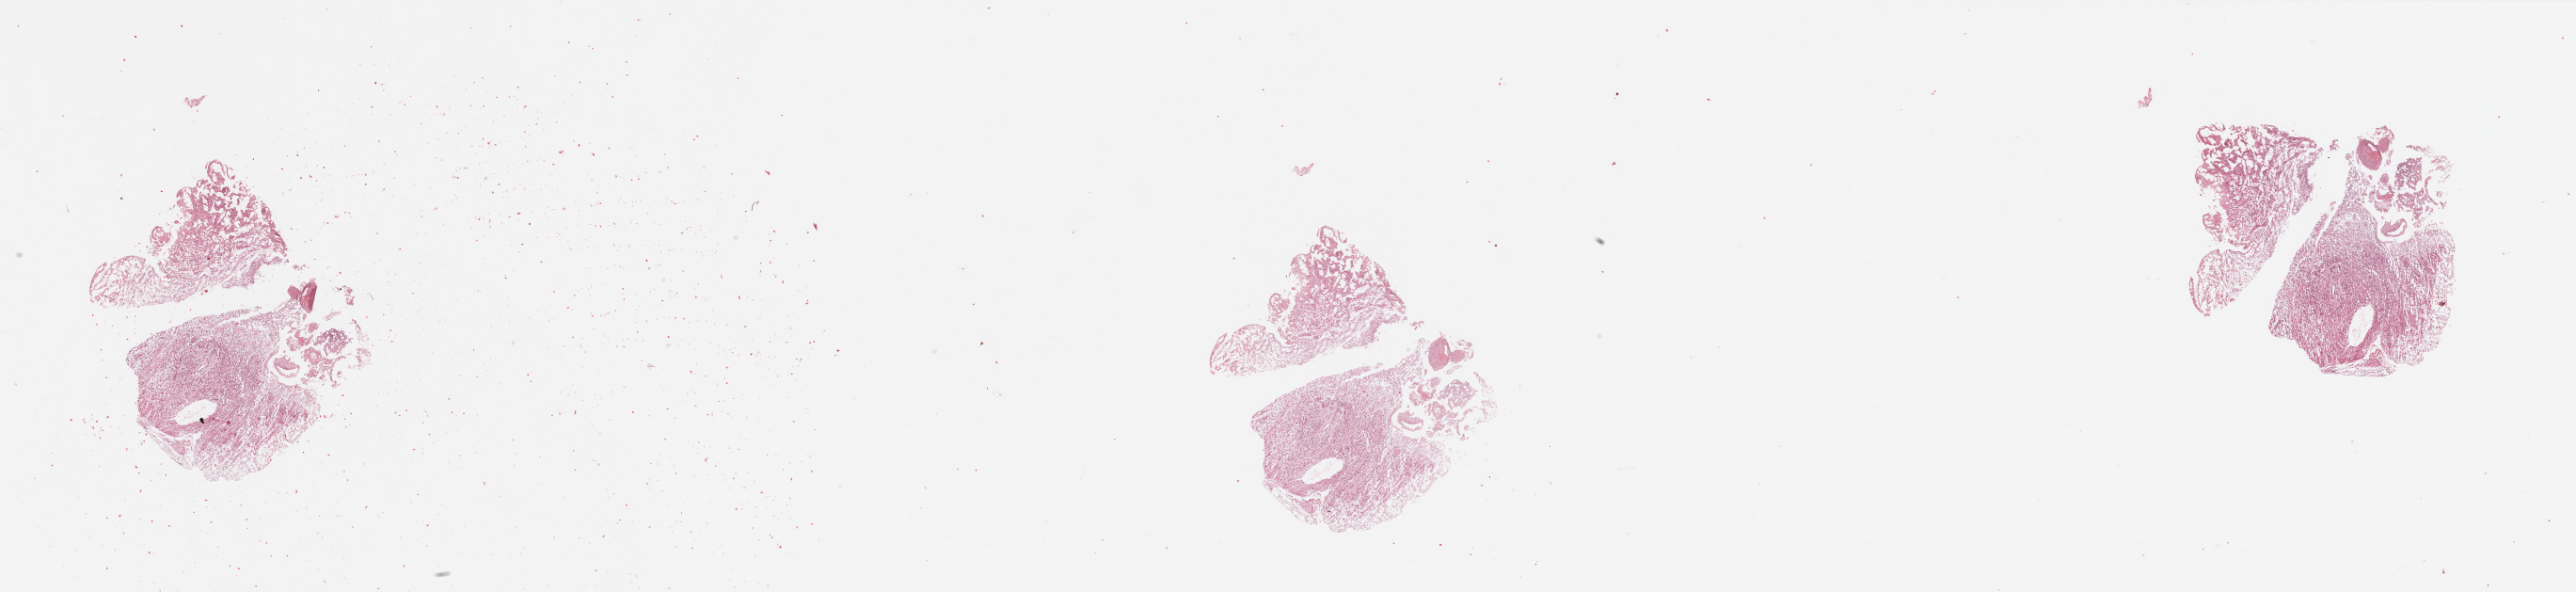
Hematoxylin and eosin (H&E) stained whole-slide image — low-resolution overview of the scanned area, about 43.3 x 10.0 mm (acquisition: 20x scan); tumour tissue sample, sampled site: brain. 65-year-old female patient. Composition of this section per pathologist review: tumour nuclei 80%, necrosis 10%.
- histologic diagnosis: Glioblastoma
- primary tumour site (as recorded): temporal lobe